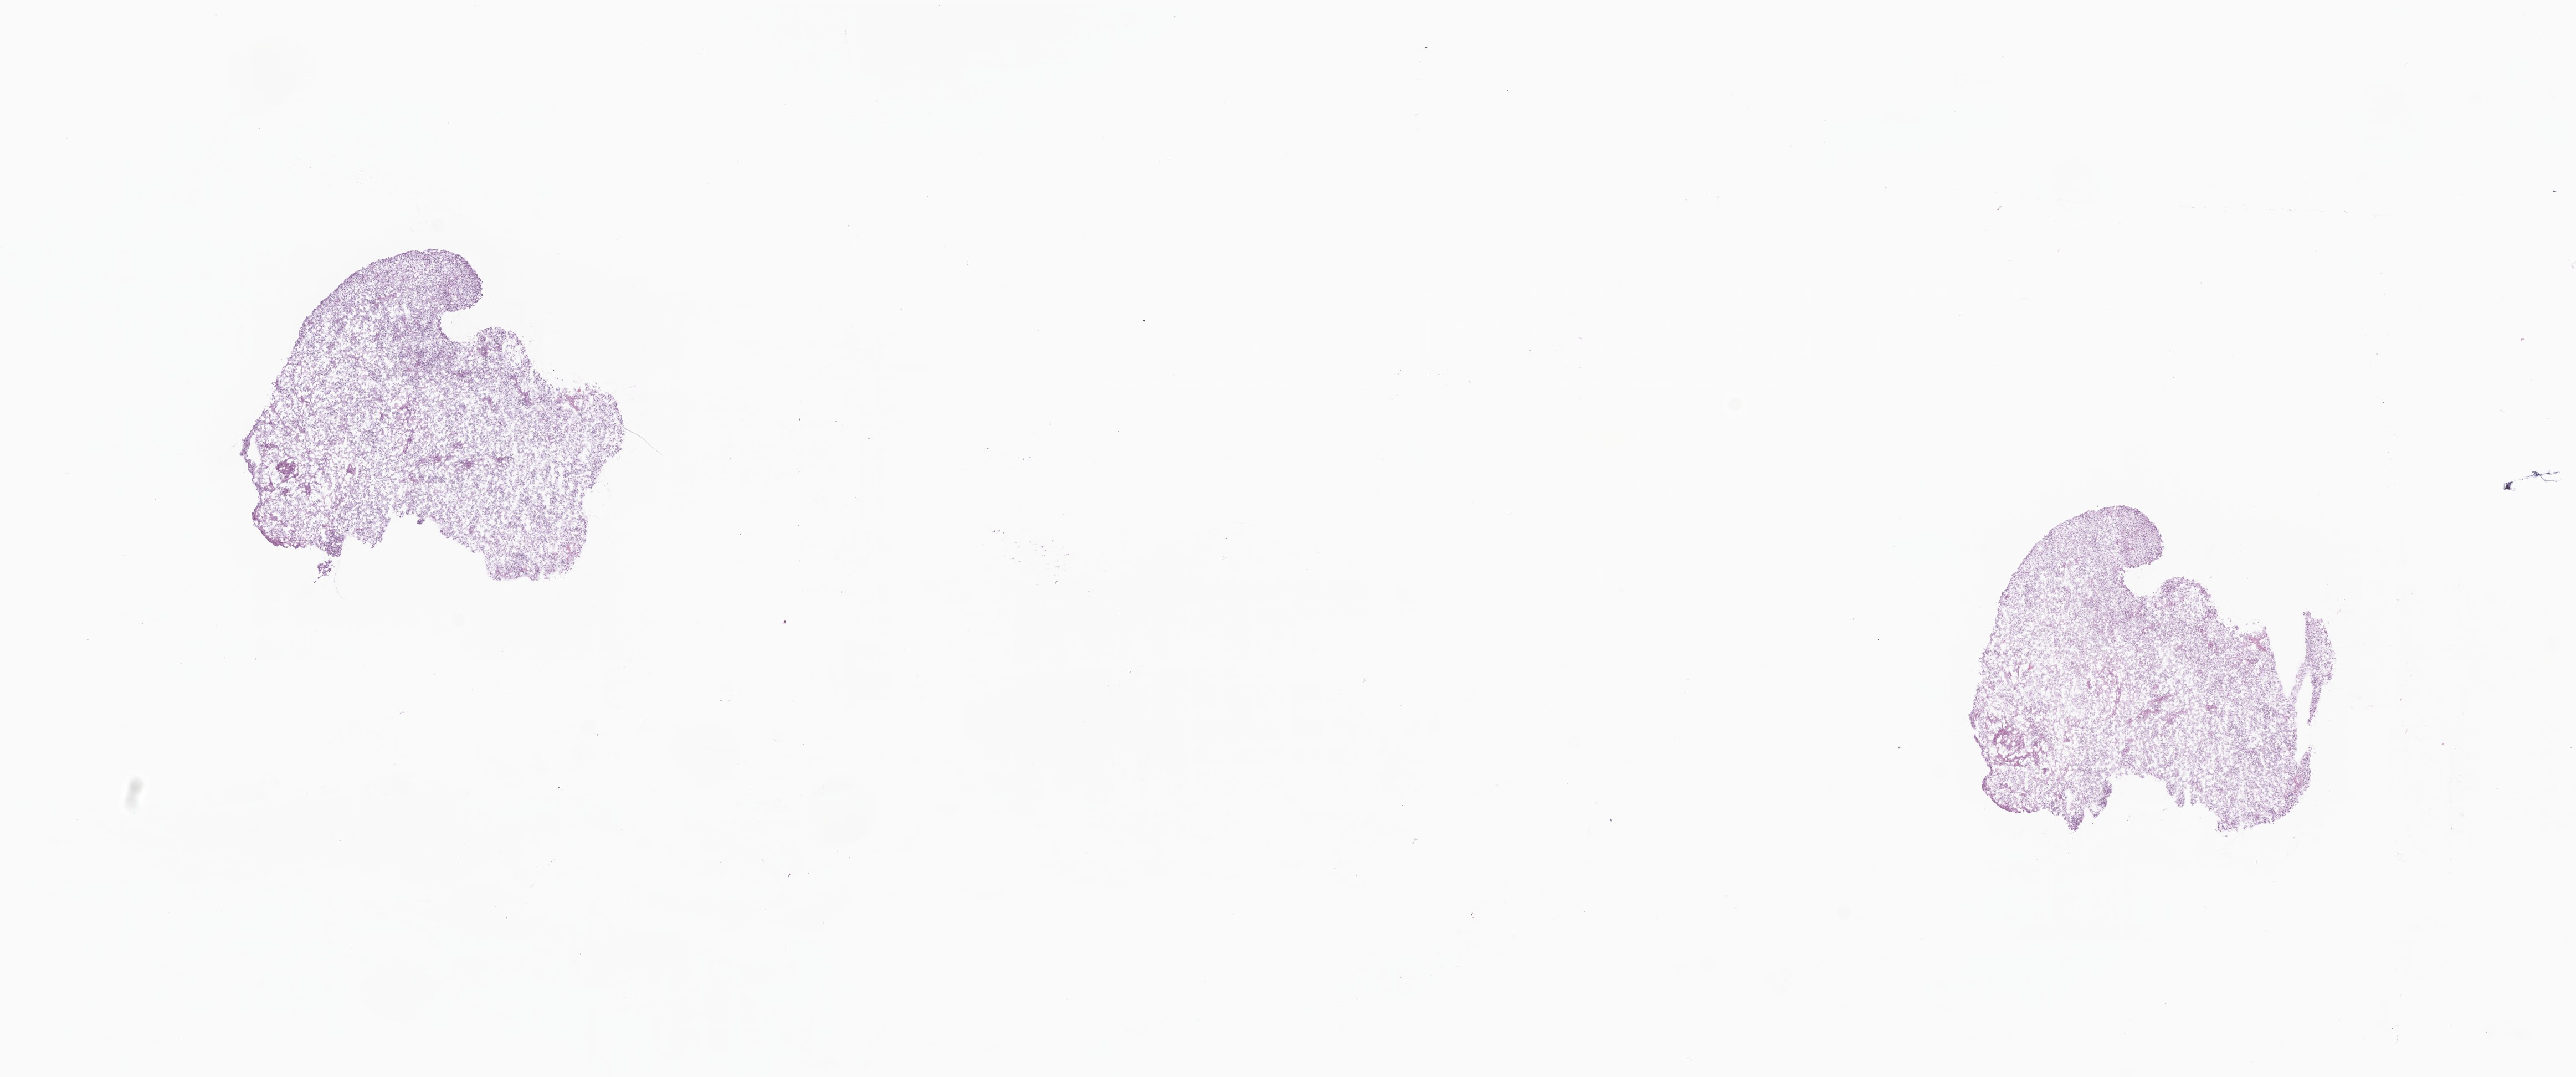
H&E whole-slide image, whole scanned area (about 19.6 x 8.2 mm) shown as a low-resolution overview, frozen section, specimen: primary tumor, anatomic site: brain. Female, age 78 years at initial diagnosis. Composition of this section per pathologist review: tumor cells 100%, tumor nuclei 97%, stromal cells 0%, necrosis 0%, normal cells 0%. Infiltration values recorded for this section: lymphocyte infiltration 0%, monocyte infiltration 0%, neutrophil infiltration 0%.
Diagnosis: Glioblastoma, NOS. Section: bottom of the tissue portion.